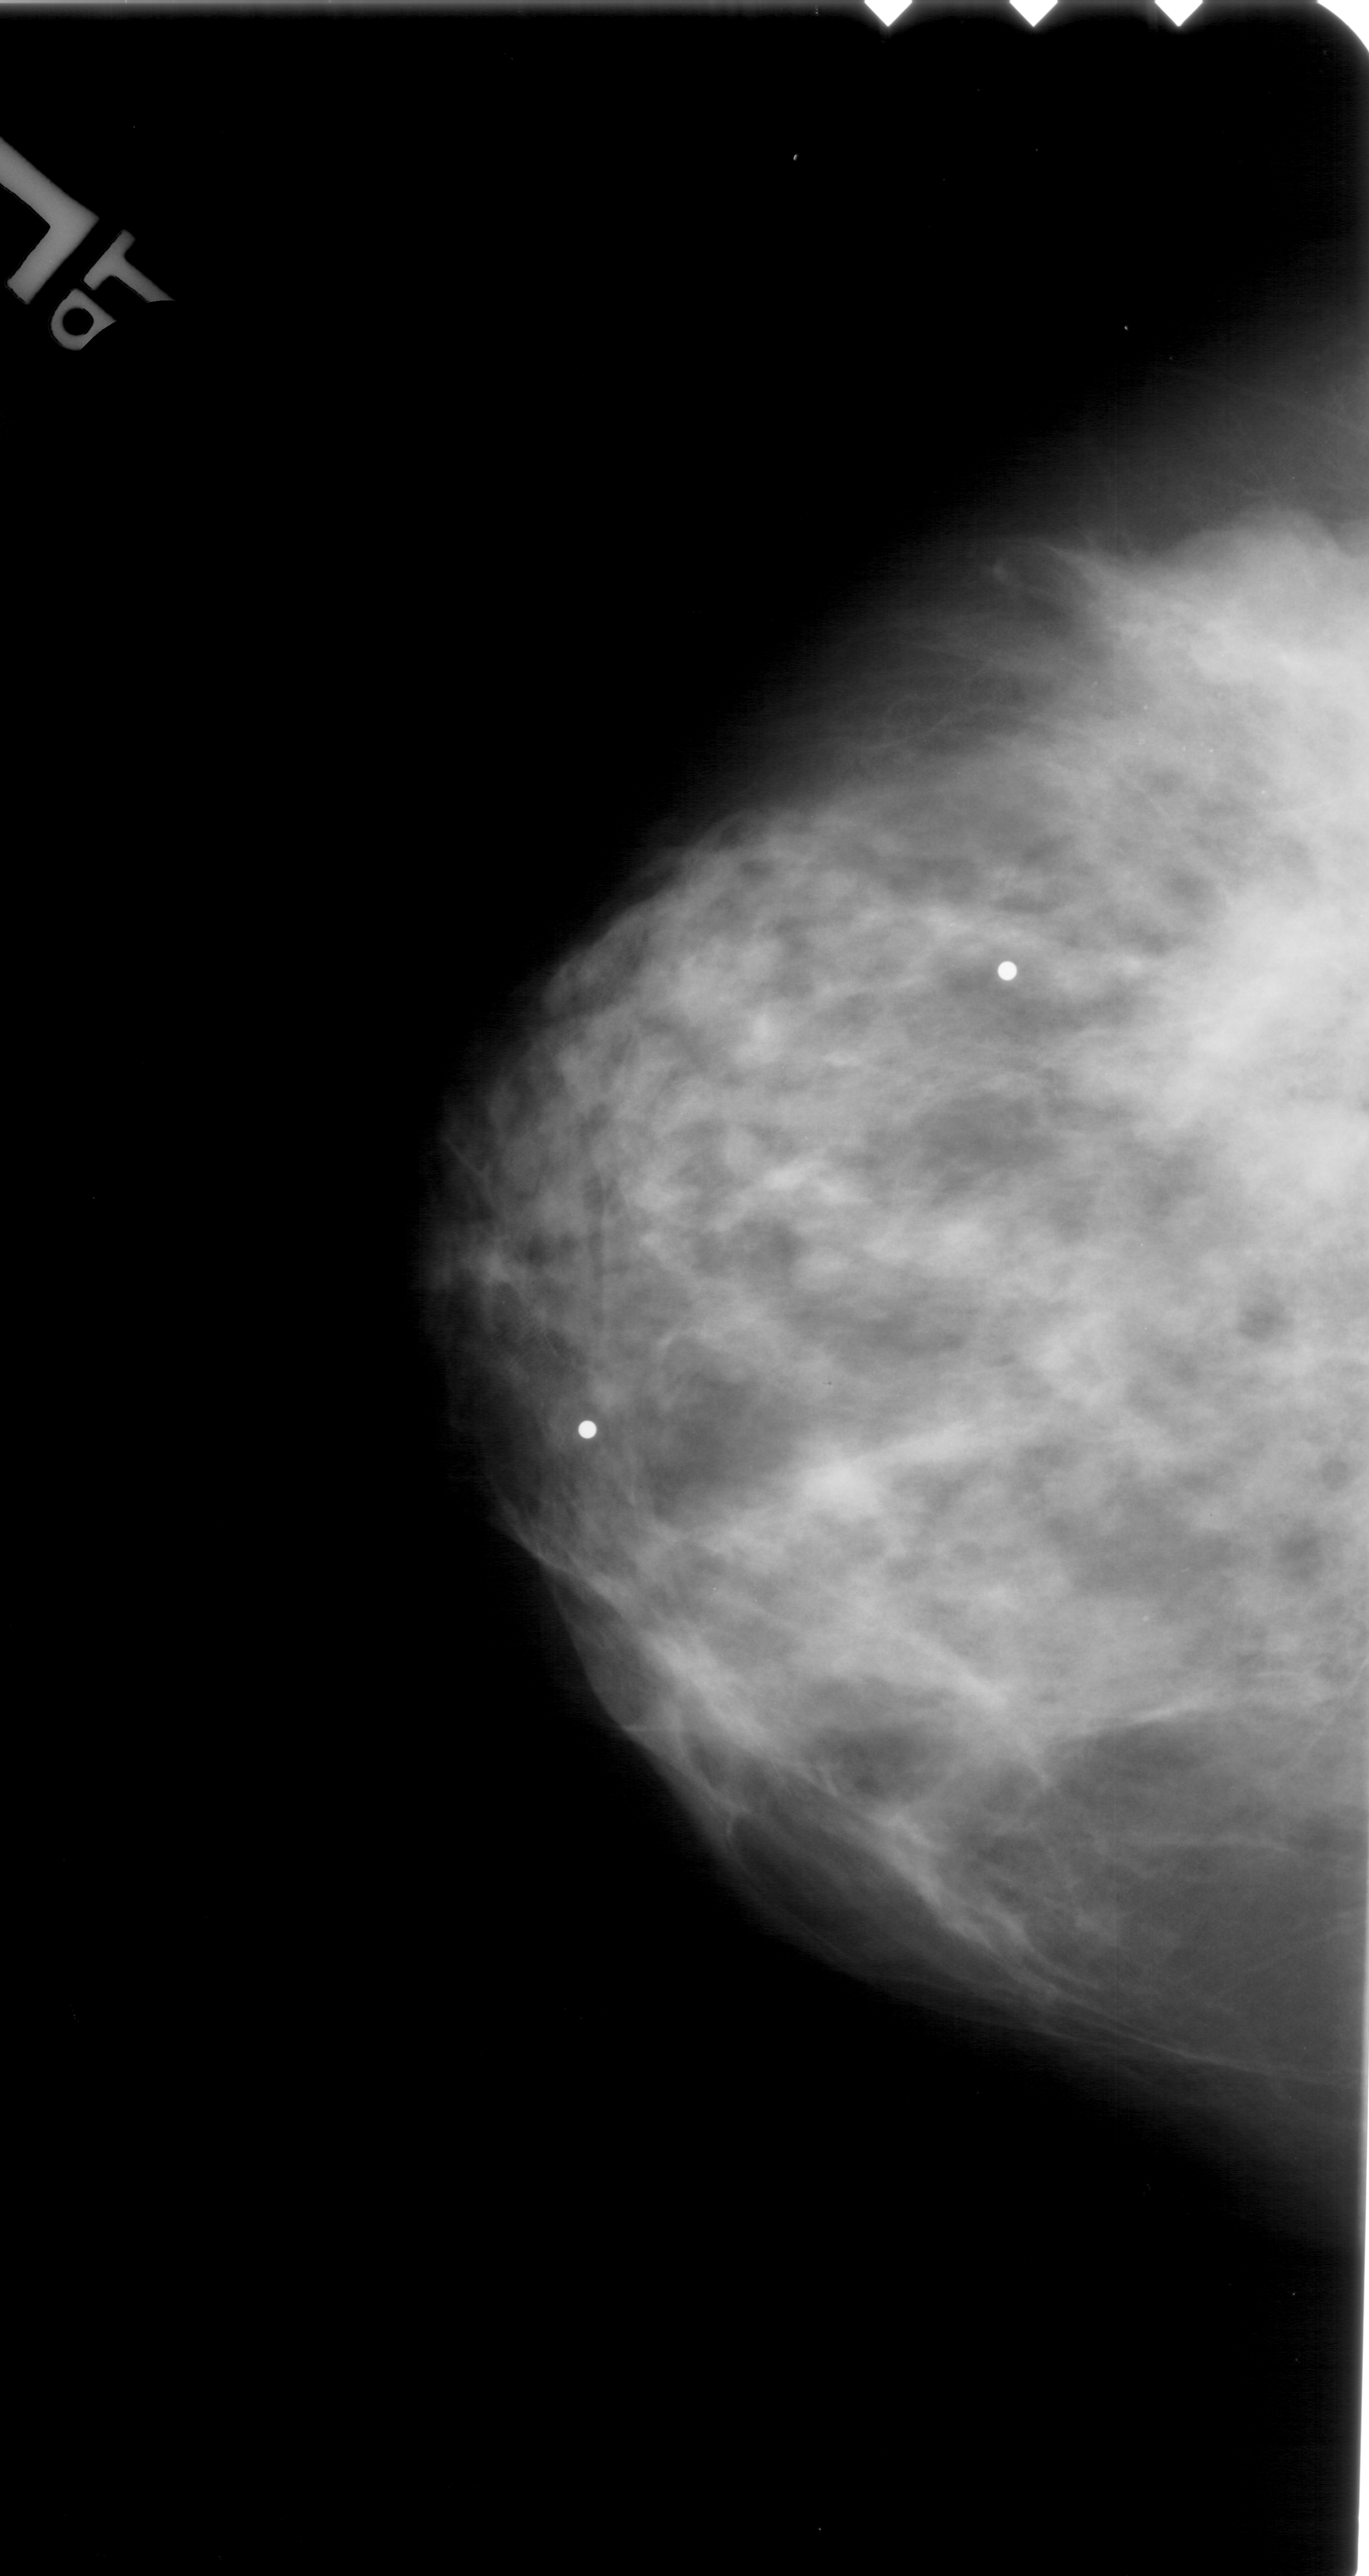
Mammogram (digitized film); left breast; craniocaudal (CC) view; breast composition: extremely dense (BI-RADS density category 4 of 4).
Marked findings (only marked abnormalities are described; nothing is implied about the rest of the image): calcifications, morphology amorphous, distribution clustered; BI-RADS assessment category 4; subtlety rating 1 on a 1 (subtle) to 5 (obvious) scale; pathology (as recorded): malignant.